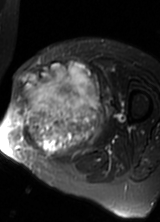
MRI of an extremity soft-tissue mass, one axial slice; slice 36 of 69 in the series (ordered by position); T2-weighted fat-saturated; MR volume resampled by the dataset authors to the PET/CT grid (not the native acquisition matrix); 3.27 mm slice thickness; 160 × 222 image matrix, field of view 156 × 217 mm. Female patient. Case-level facts recorded for this patient, not image findings: histological type: pleomorphic leiomyosarcoma; grade: high; site of the primary tumour: left thigh.
Structures marked on this image (expert contour drawn on MRI and transferred to this co-registered scan by the dataset authors):
- gross tumour volume including surrounding oedema: bounding box [x1, y1, x2, y2] px = [16, 61, 108, 160]
- gross tumour volume (mass): [16, 61, 103, 158]